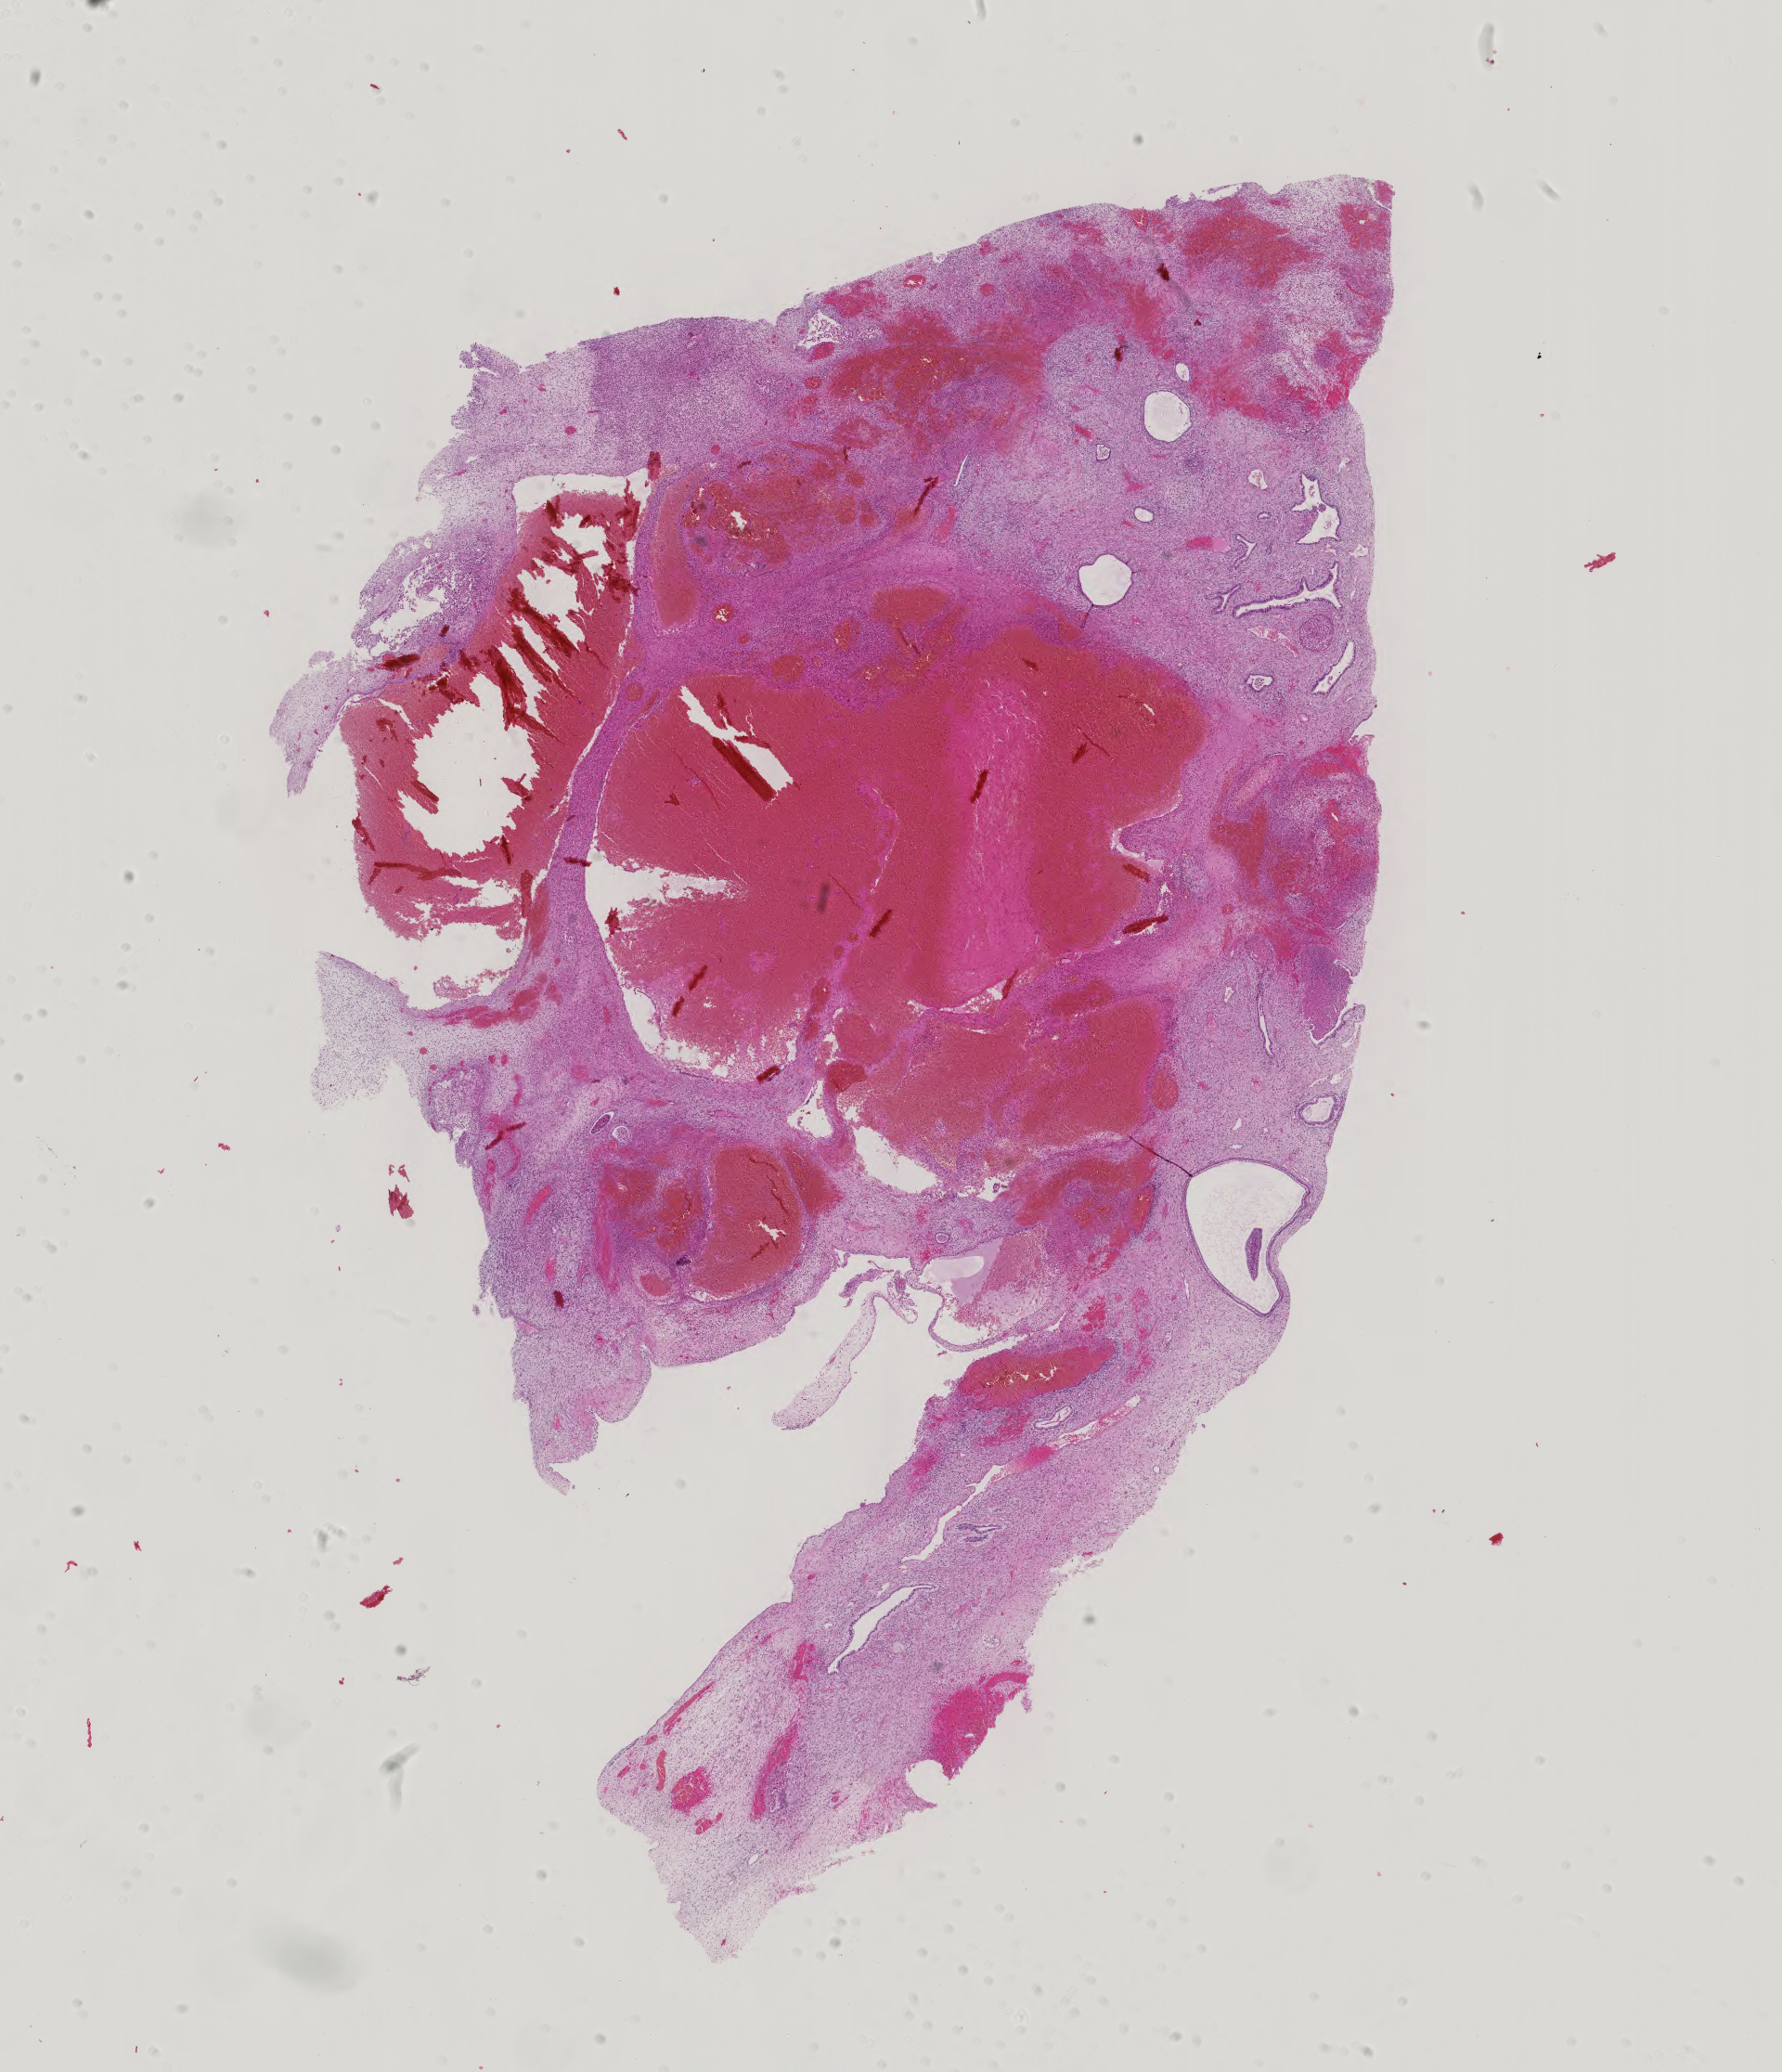
Digitized Hematoxylin and eosin (H&E) stained tissue section (whole slide) — shown as a low-resolution overview of the whole scanned area (about 14.0 x 16.3 mm, from a 40x scan). Patient sex: male.
• specimen: formalin-fixed paraffin-embedded (FFPE) diagnostic section; primary tumour sample from the testis